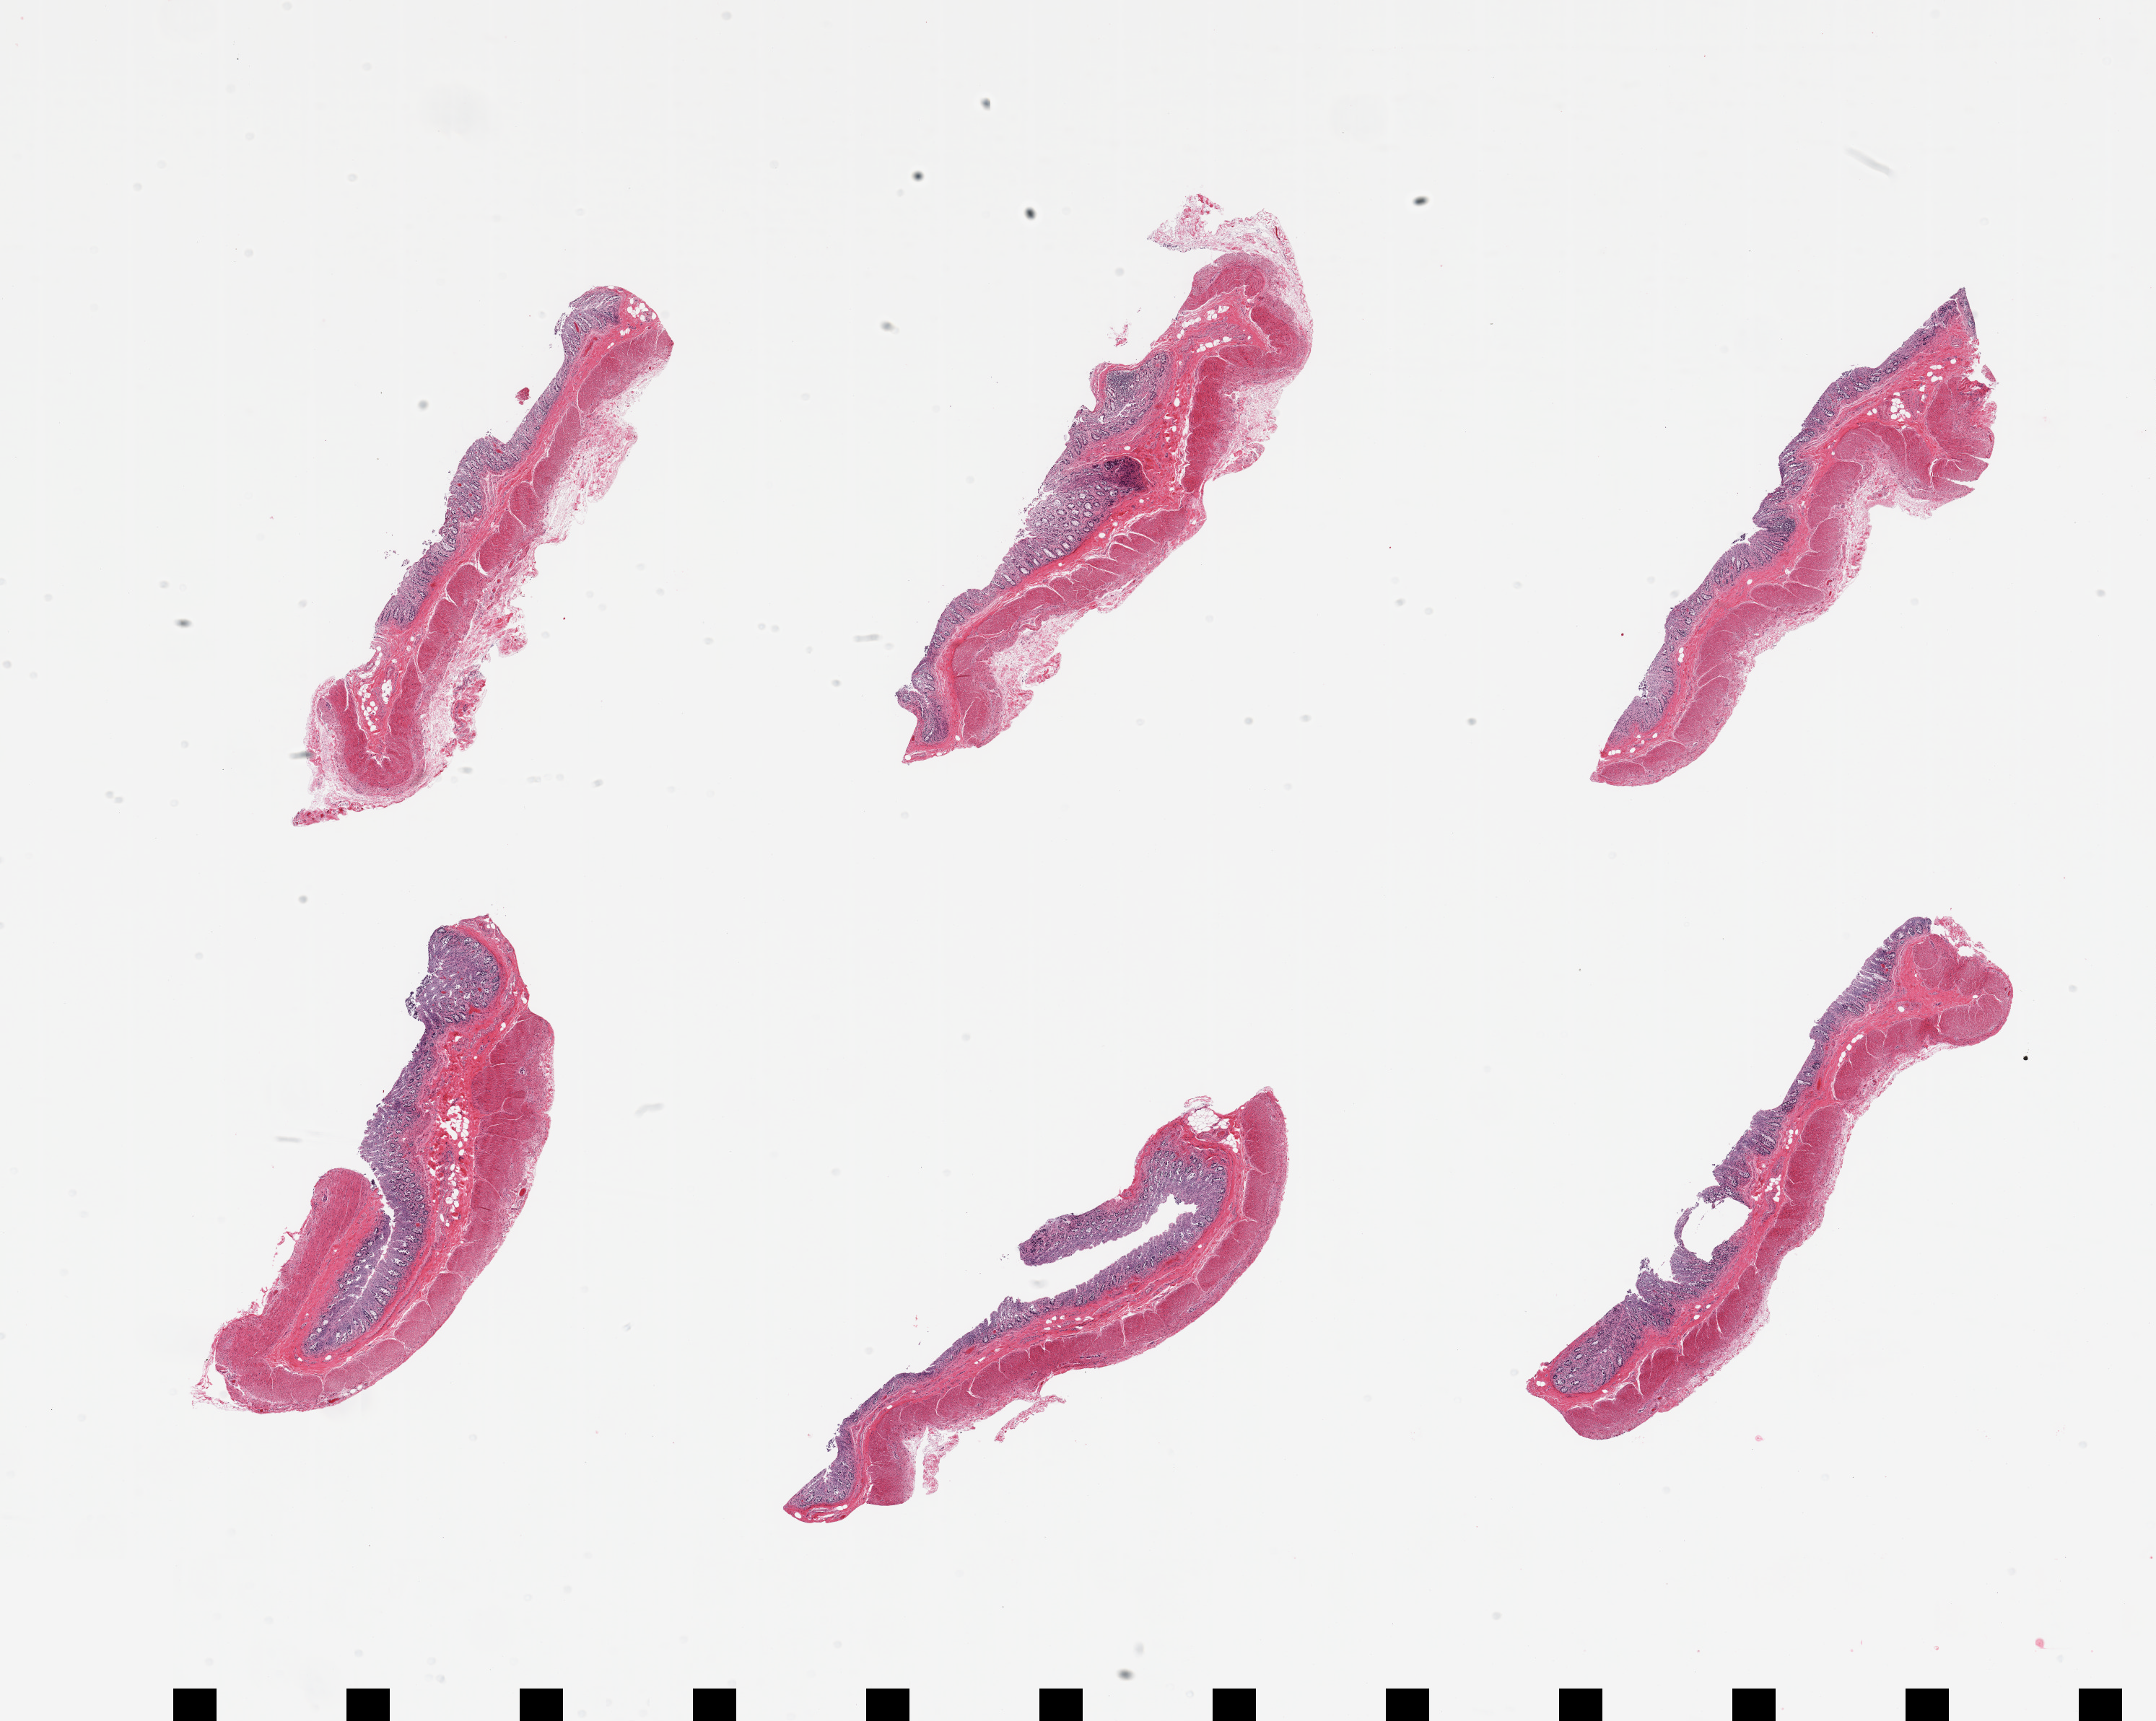
Digitized hematoxylin and eosin (H&E)-stained section, shown as a low-resolution overview of the whole scanned area (about 23.6 x 18.9 mm); PAXgene-fixed paraffin-embedded (PFPE) section; section of transverse colon (target tissue); donor tissue sample. Donor: male.
Reviewer comment on this tissue sample: 6 pieces; glands largely autolyzed, muscle intact.